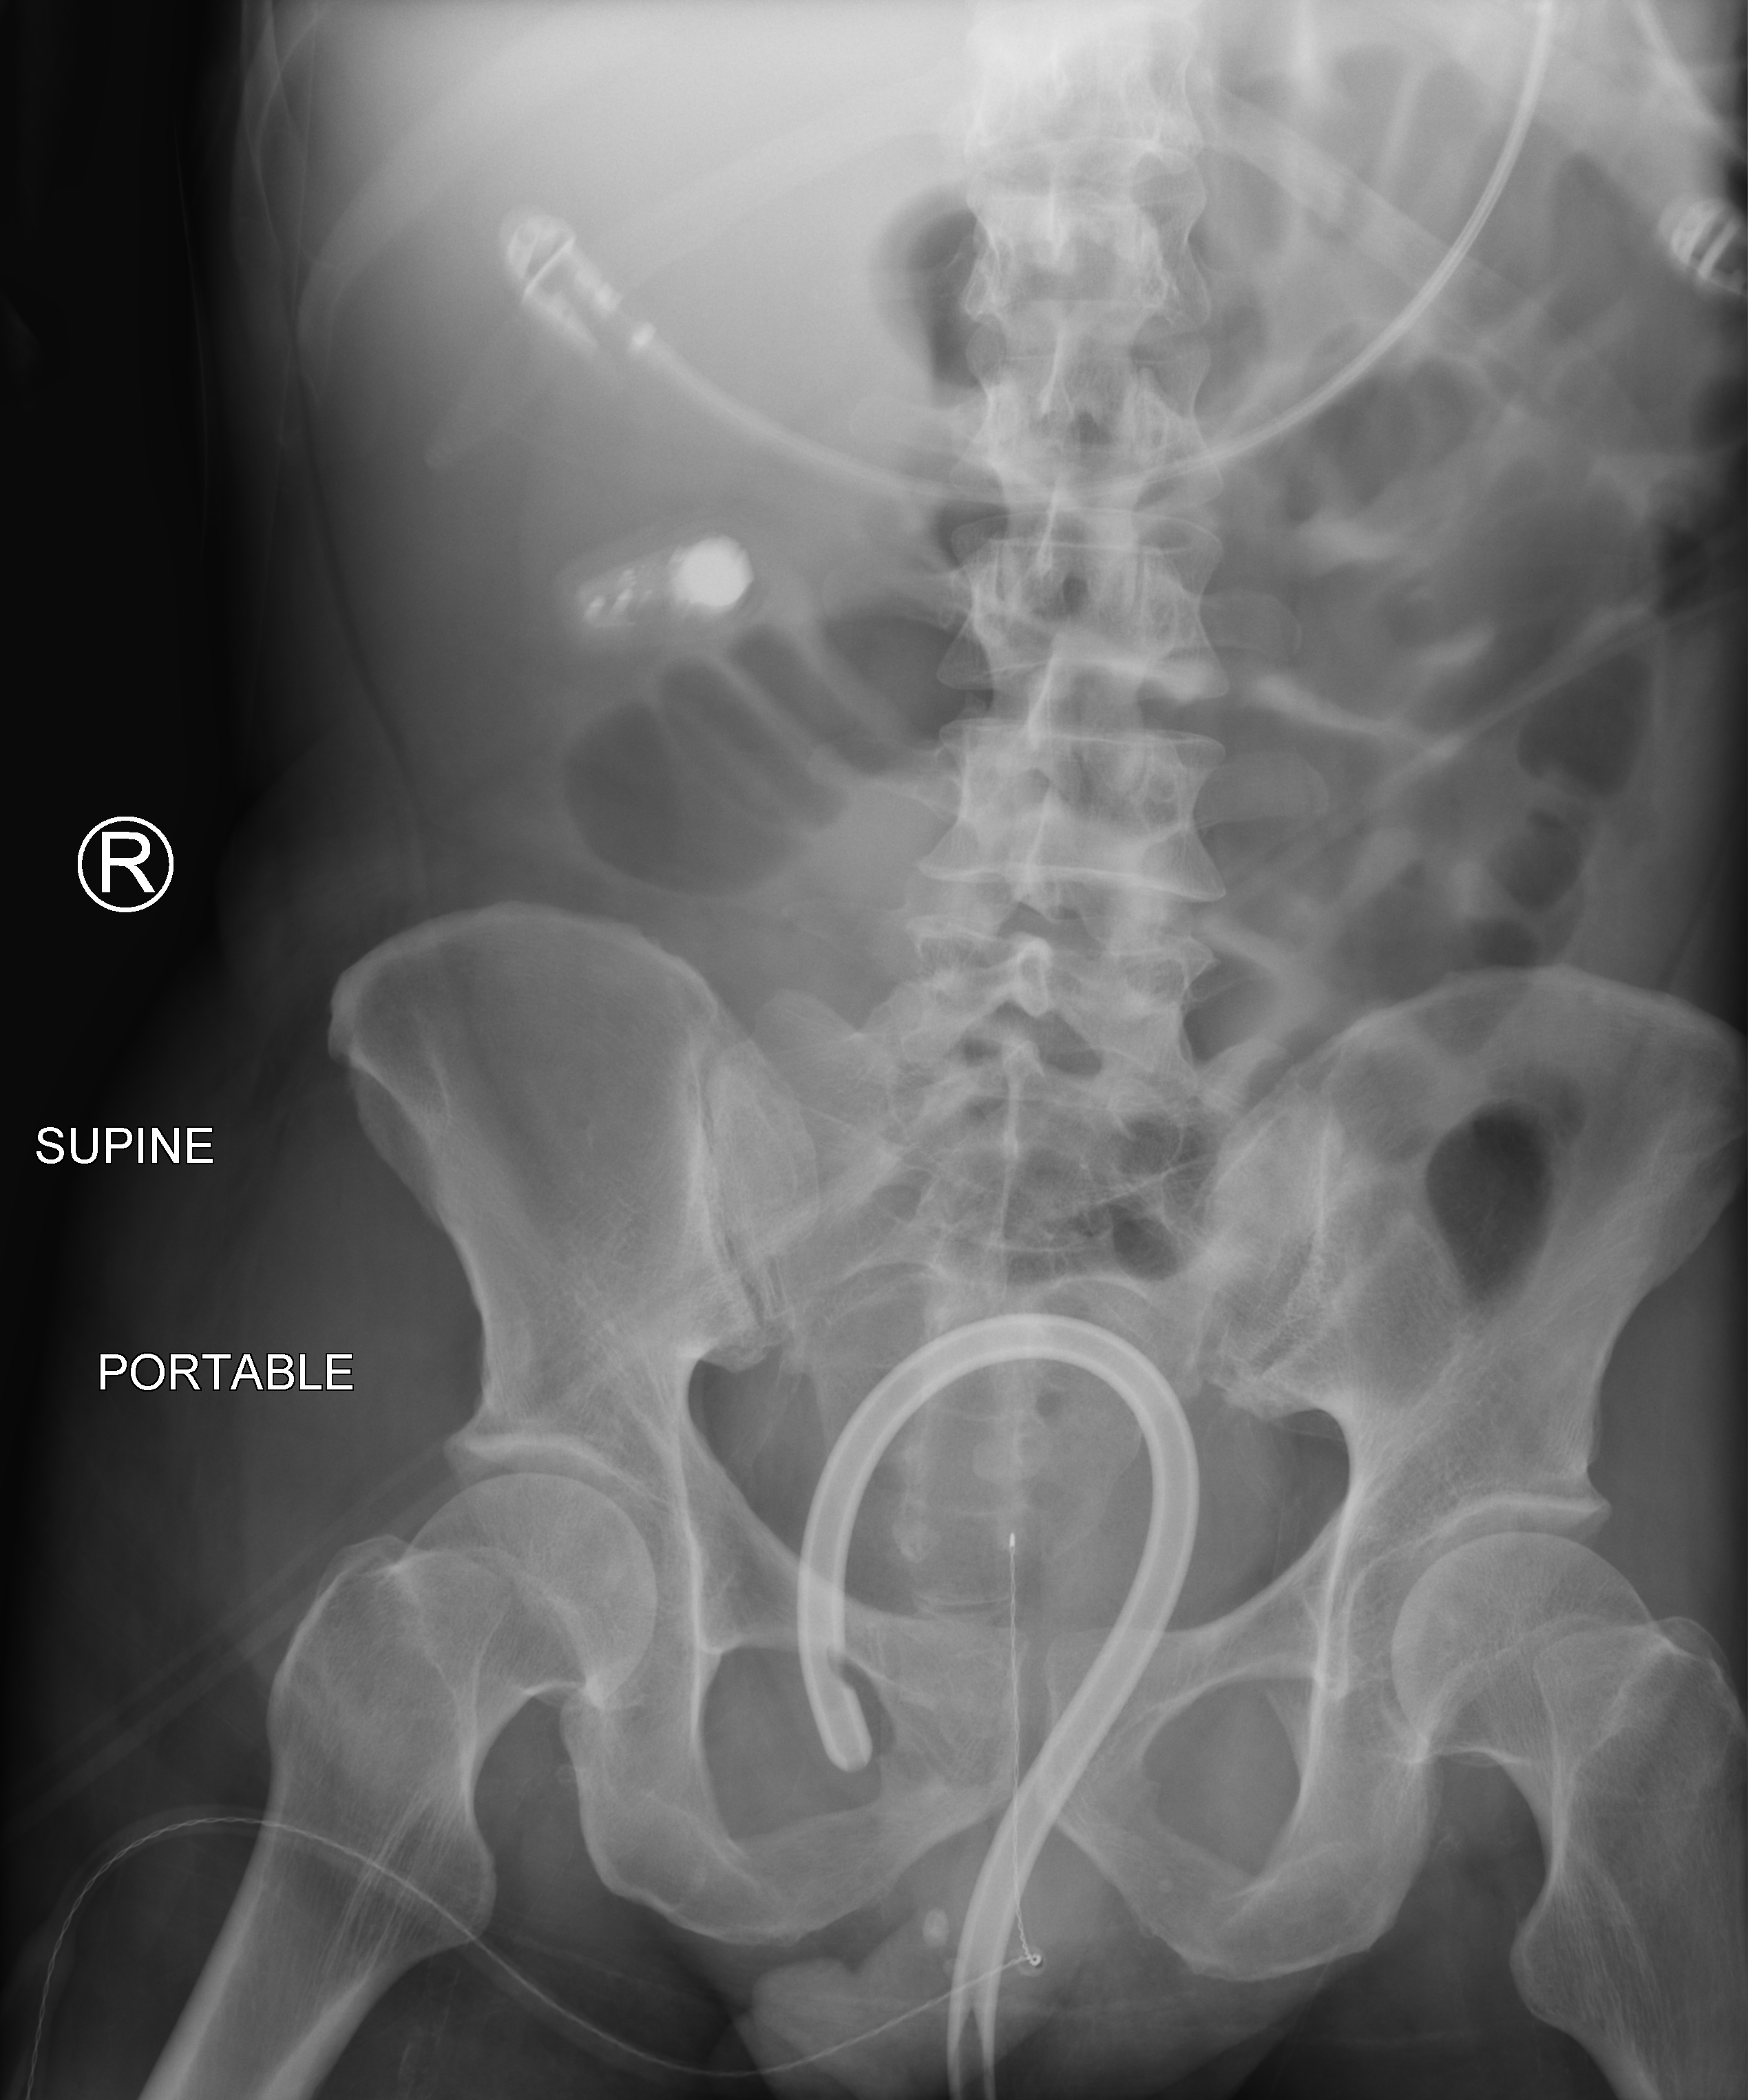
Abdomen X-ray (portable); anteroposterior (AP) projection. Male patient hospitalised with COVID-19, age 18–59 years.
Hospital-stay facts (about this admission, not read from this image; timing relative to this image not recorded): mechanically ventilated during this hospital stay: yes; hypertension (admission record): yes; admitted to intensive care during this hospital stay: yes.